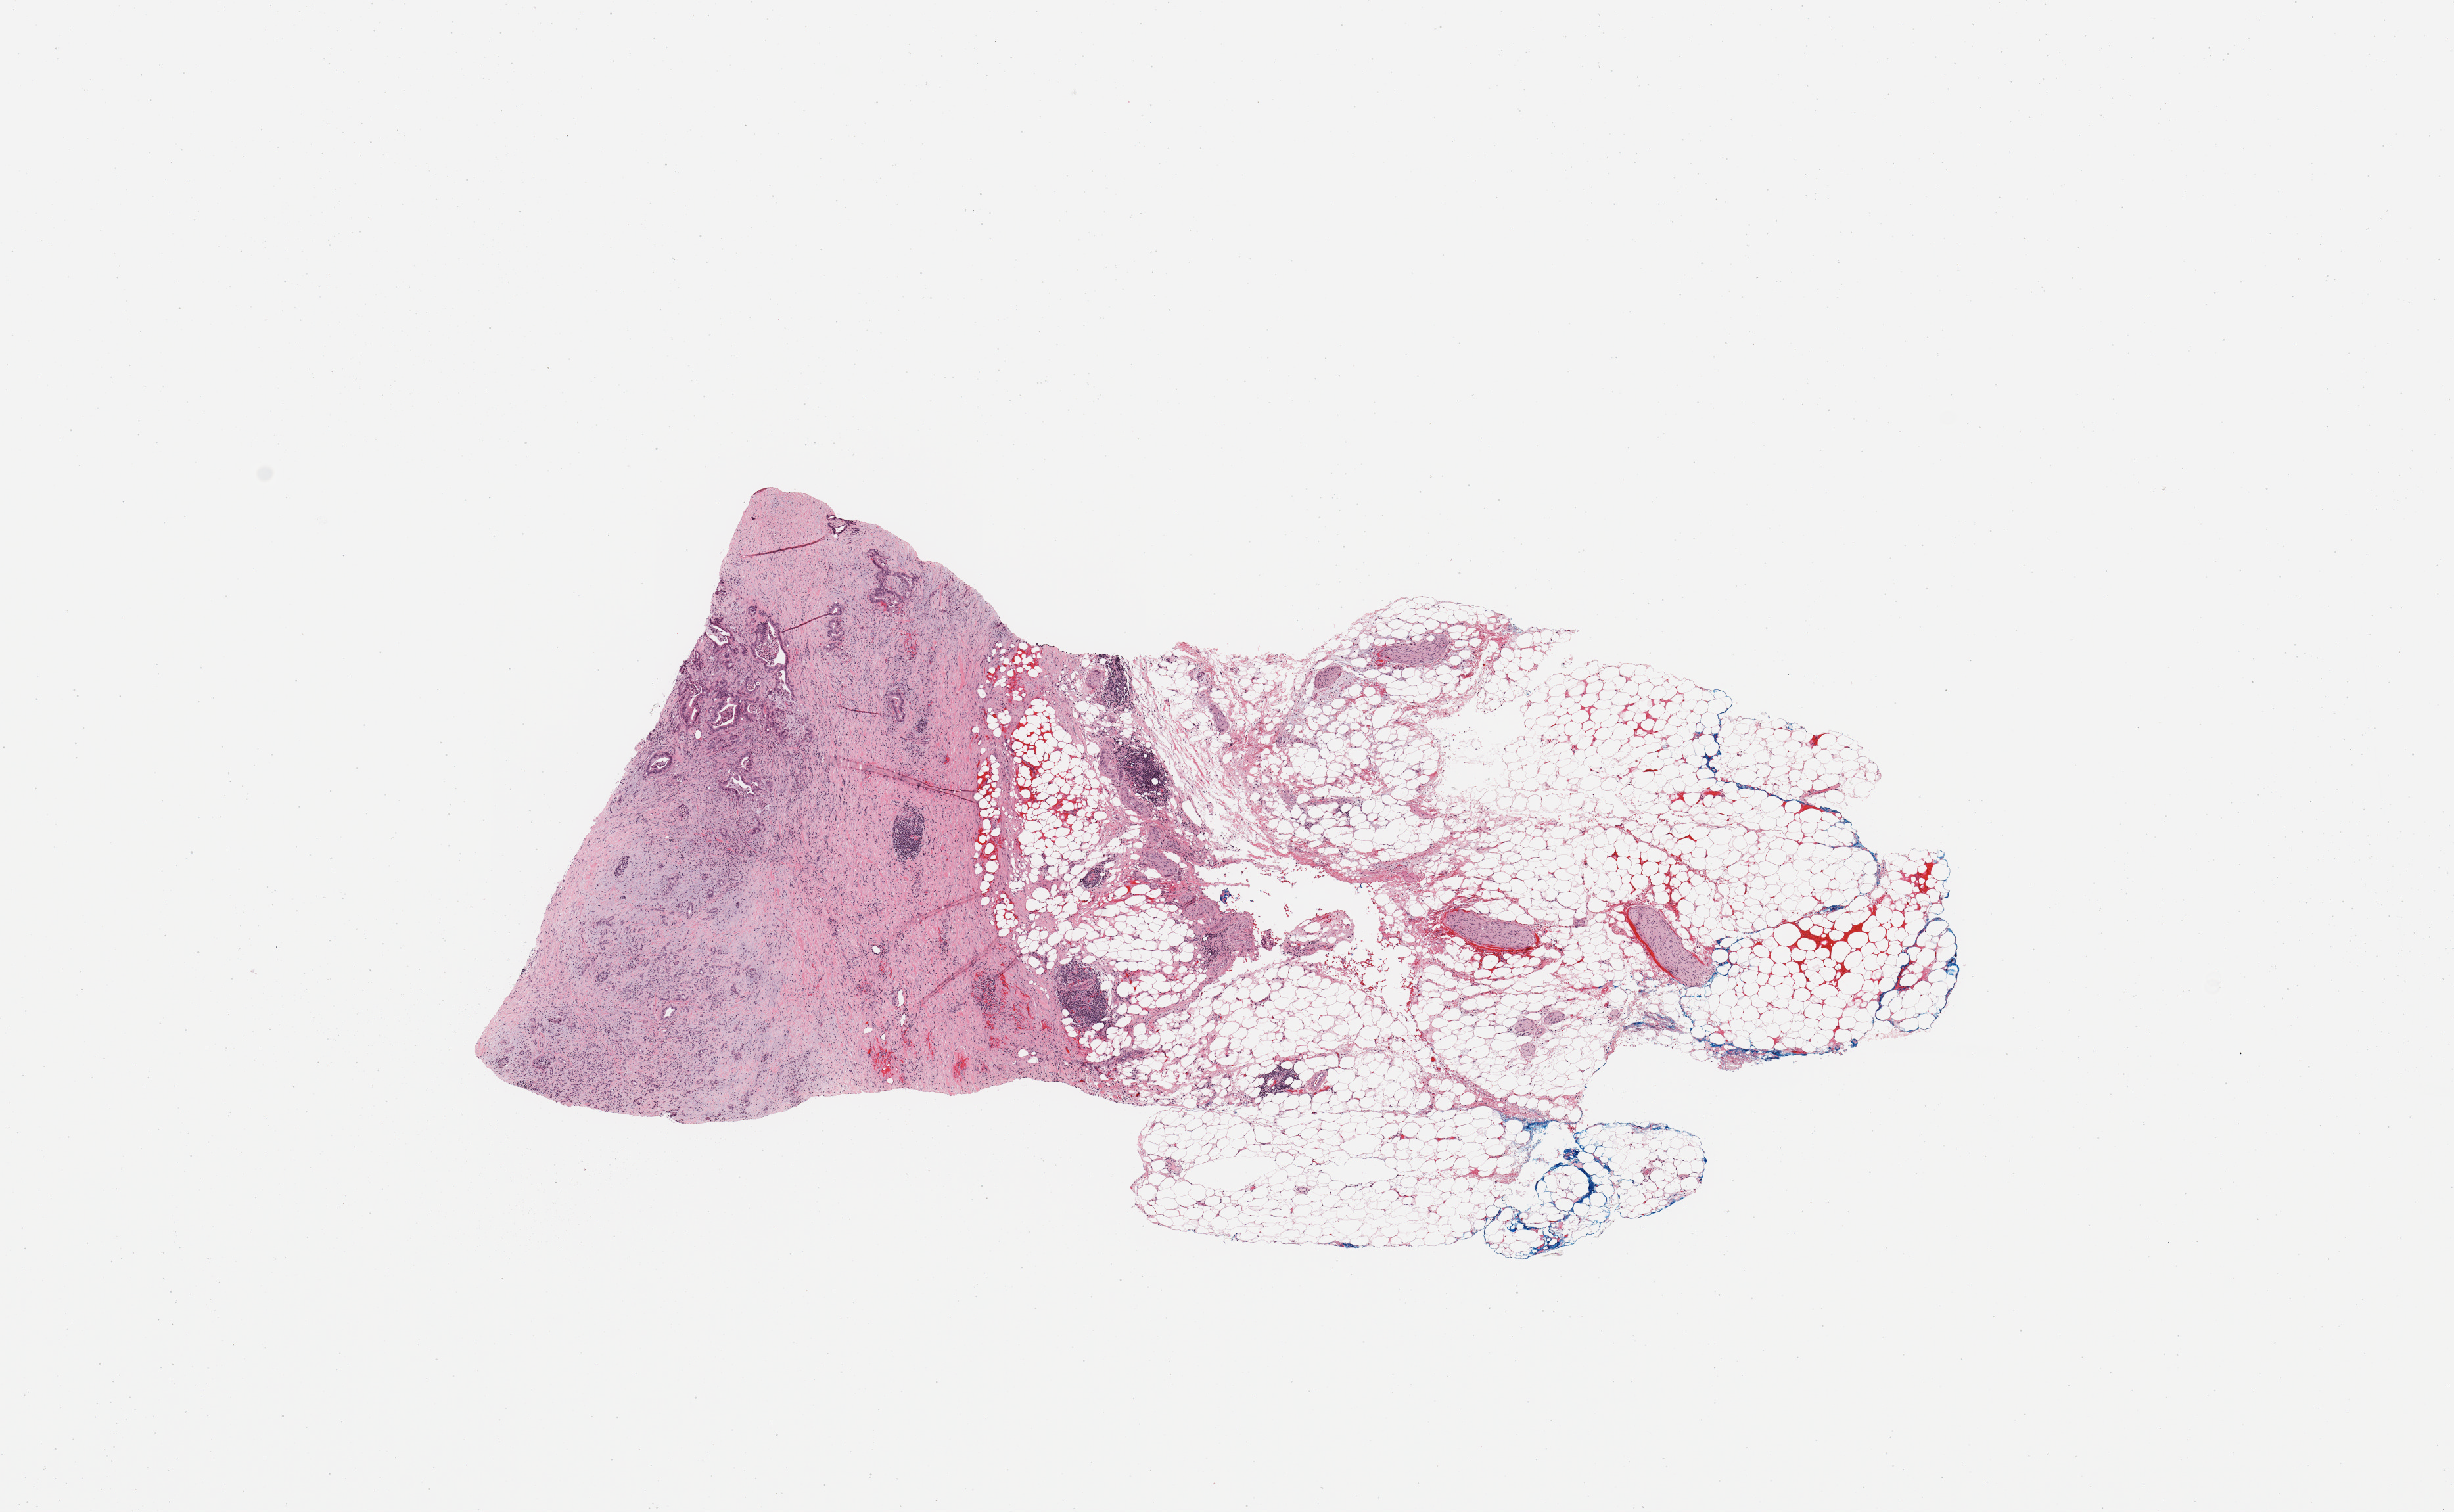
Whole-slide histology image, Hematoxylin and eosin (H&E) stained, shown as a low-resolution overview of the whole scanned area (about 14.8 x 9.1 mm, slide scanned at 20x); tumour tissue sample, pancreas. Patient: female, age 58 years. Histologic grade: G1 (well differentiated).
• diagnosis: Infiltrating duct carcinoma, NOS
• AJCC pathologic stage: IIB